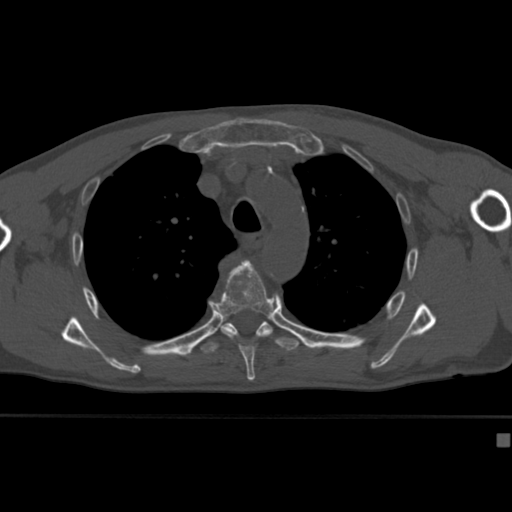
CT including the spine, one axial slice; slice 305 of 430 in the series (ordered by position); reconstruction kernel Br40s; bone window (W 1800 / L 400 HU); 1.5 mm slice thickness; 512 × 512 image matrix, field of view 337 × 337 mm. Male patient, age 64 years. Case-level facts recorded for this patient, not image findings: primary cancer: uterus.
Outlined on this slice (semi-automatically segmented with operator editing):
- T4 vertebra: box from (x=240, y=259) to (x=248, y=263) px
- T5 vertebra: (x=216, y=261)–(x=274, y=382)
- T6 vertebra: (x=200, y=321)–(x=299, y=354)